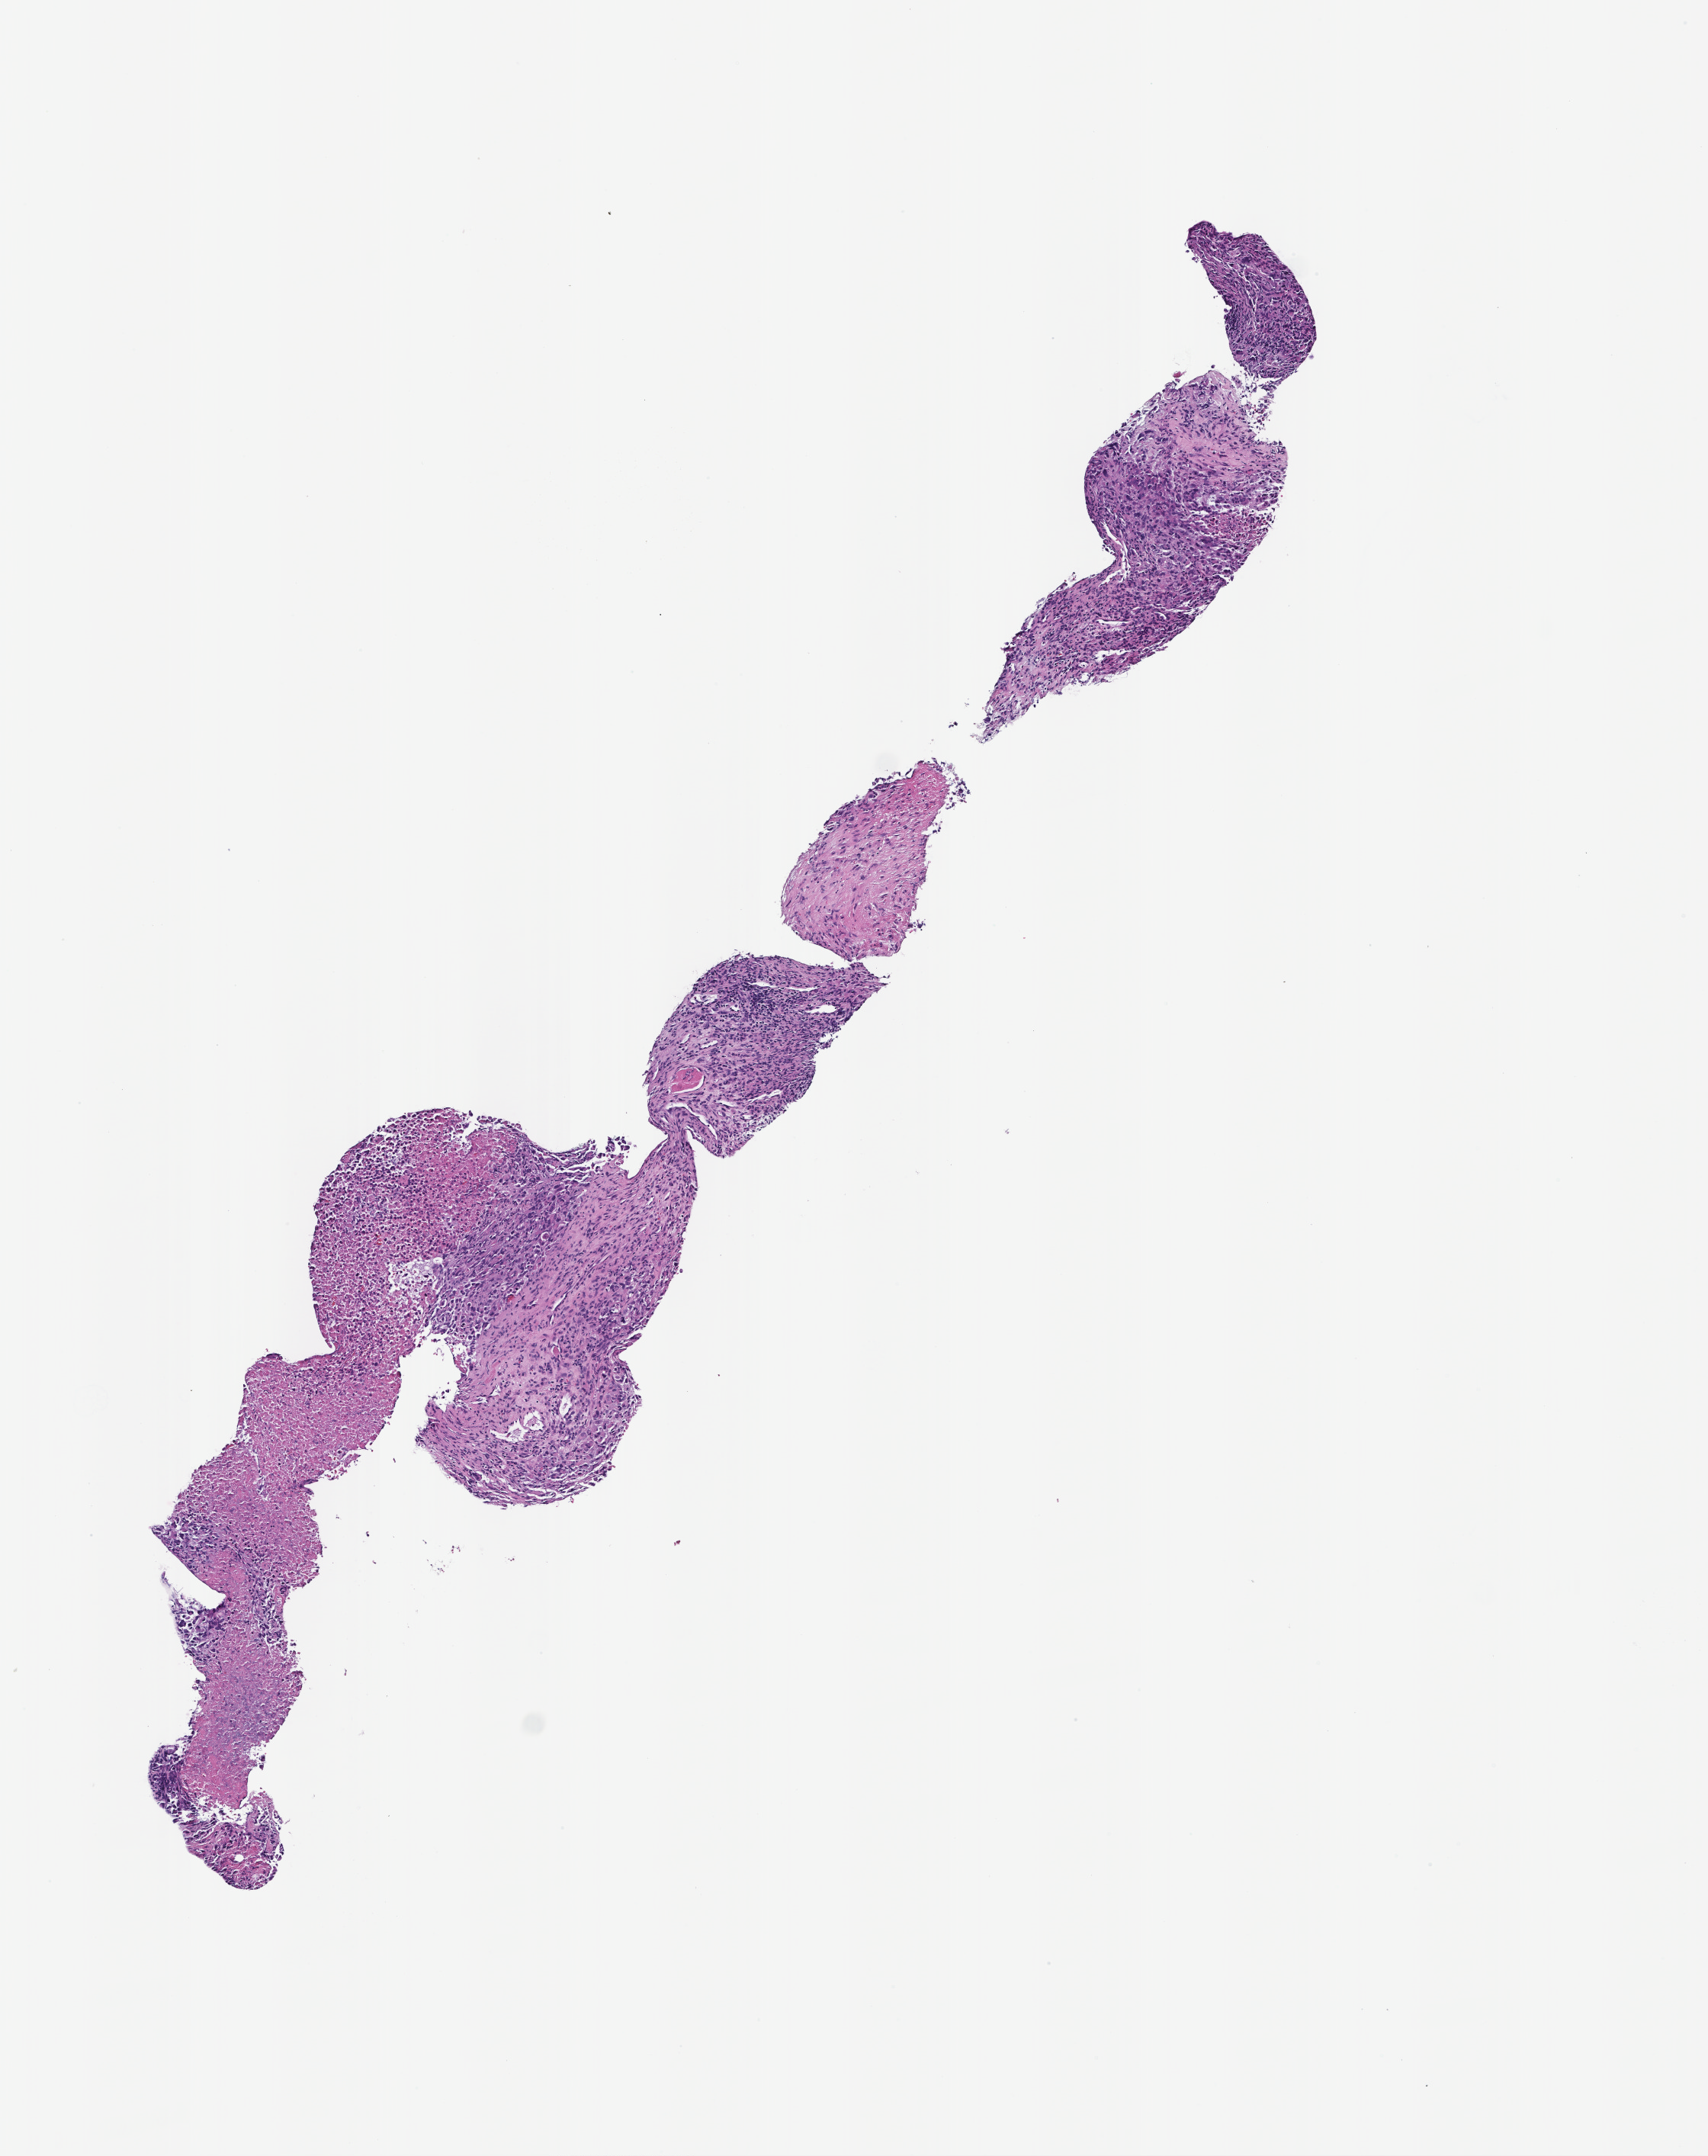
Digitized H&E-stained section — shown as a low-resolution overview of the whole scanned area (about 4.5 x 5.7 mm). Formalin-fixed, paraffin-embedded (FFPE) tissue. Patient sex: male.
This section: metastatic tumor tissue. Patient diagnosis (primary): Non-Small Cell Lung Carcinoma.